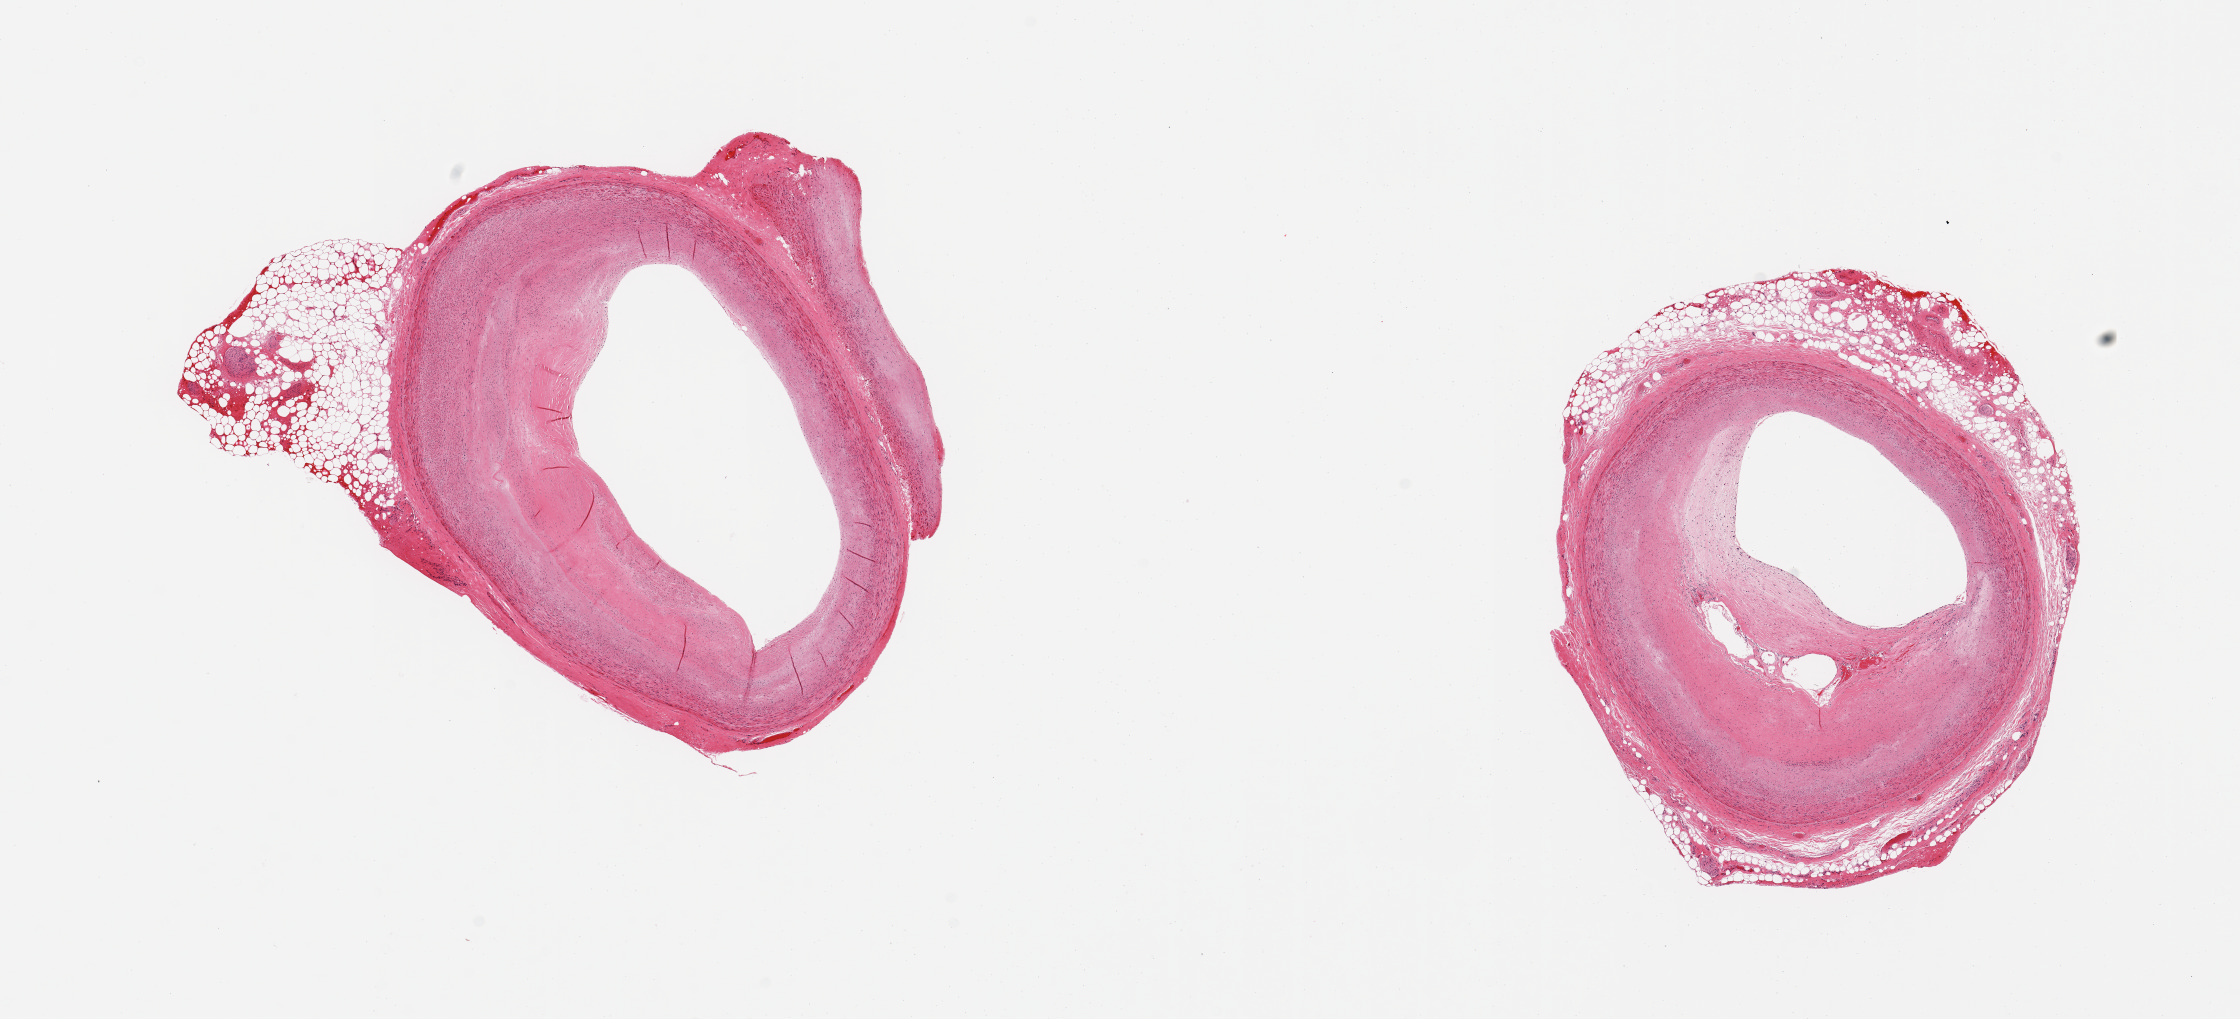
Whole-slide image, H&E stain — shown as a low-resolution overview of the whole scanned area (about 17.7 x 8.1 mm). PAXgene-fixed, paraffin-embedded tissue. Sampled site (target tissue): coronary artery. Tissue donor sample. Donor: male.
Review note (as recorded): 2 pieces; 50% to 75% luminal occlusion by atherosclerotic plaque; rim of adherent fat up to 1.66mm.